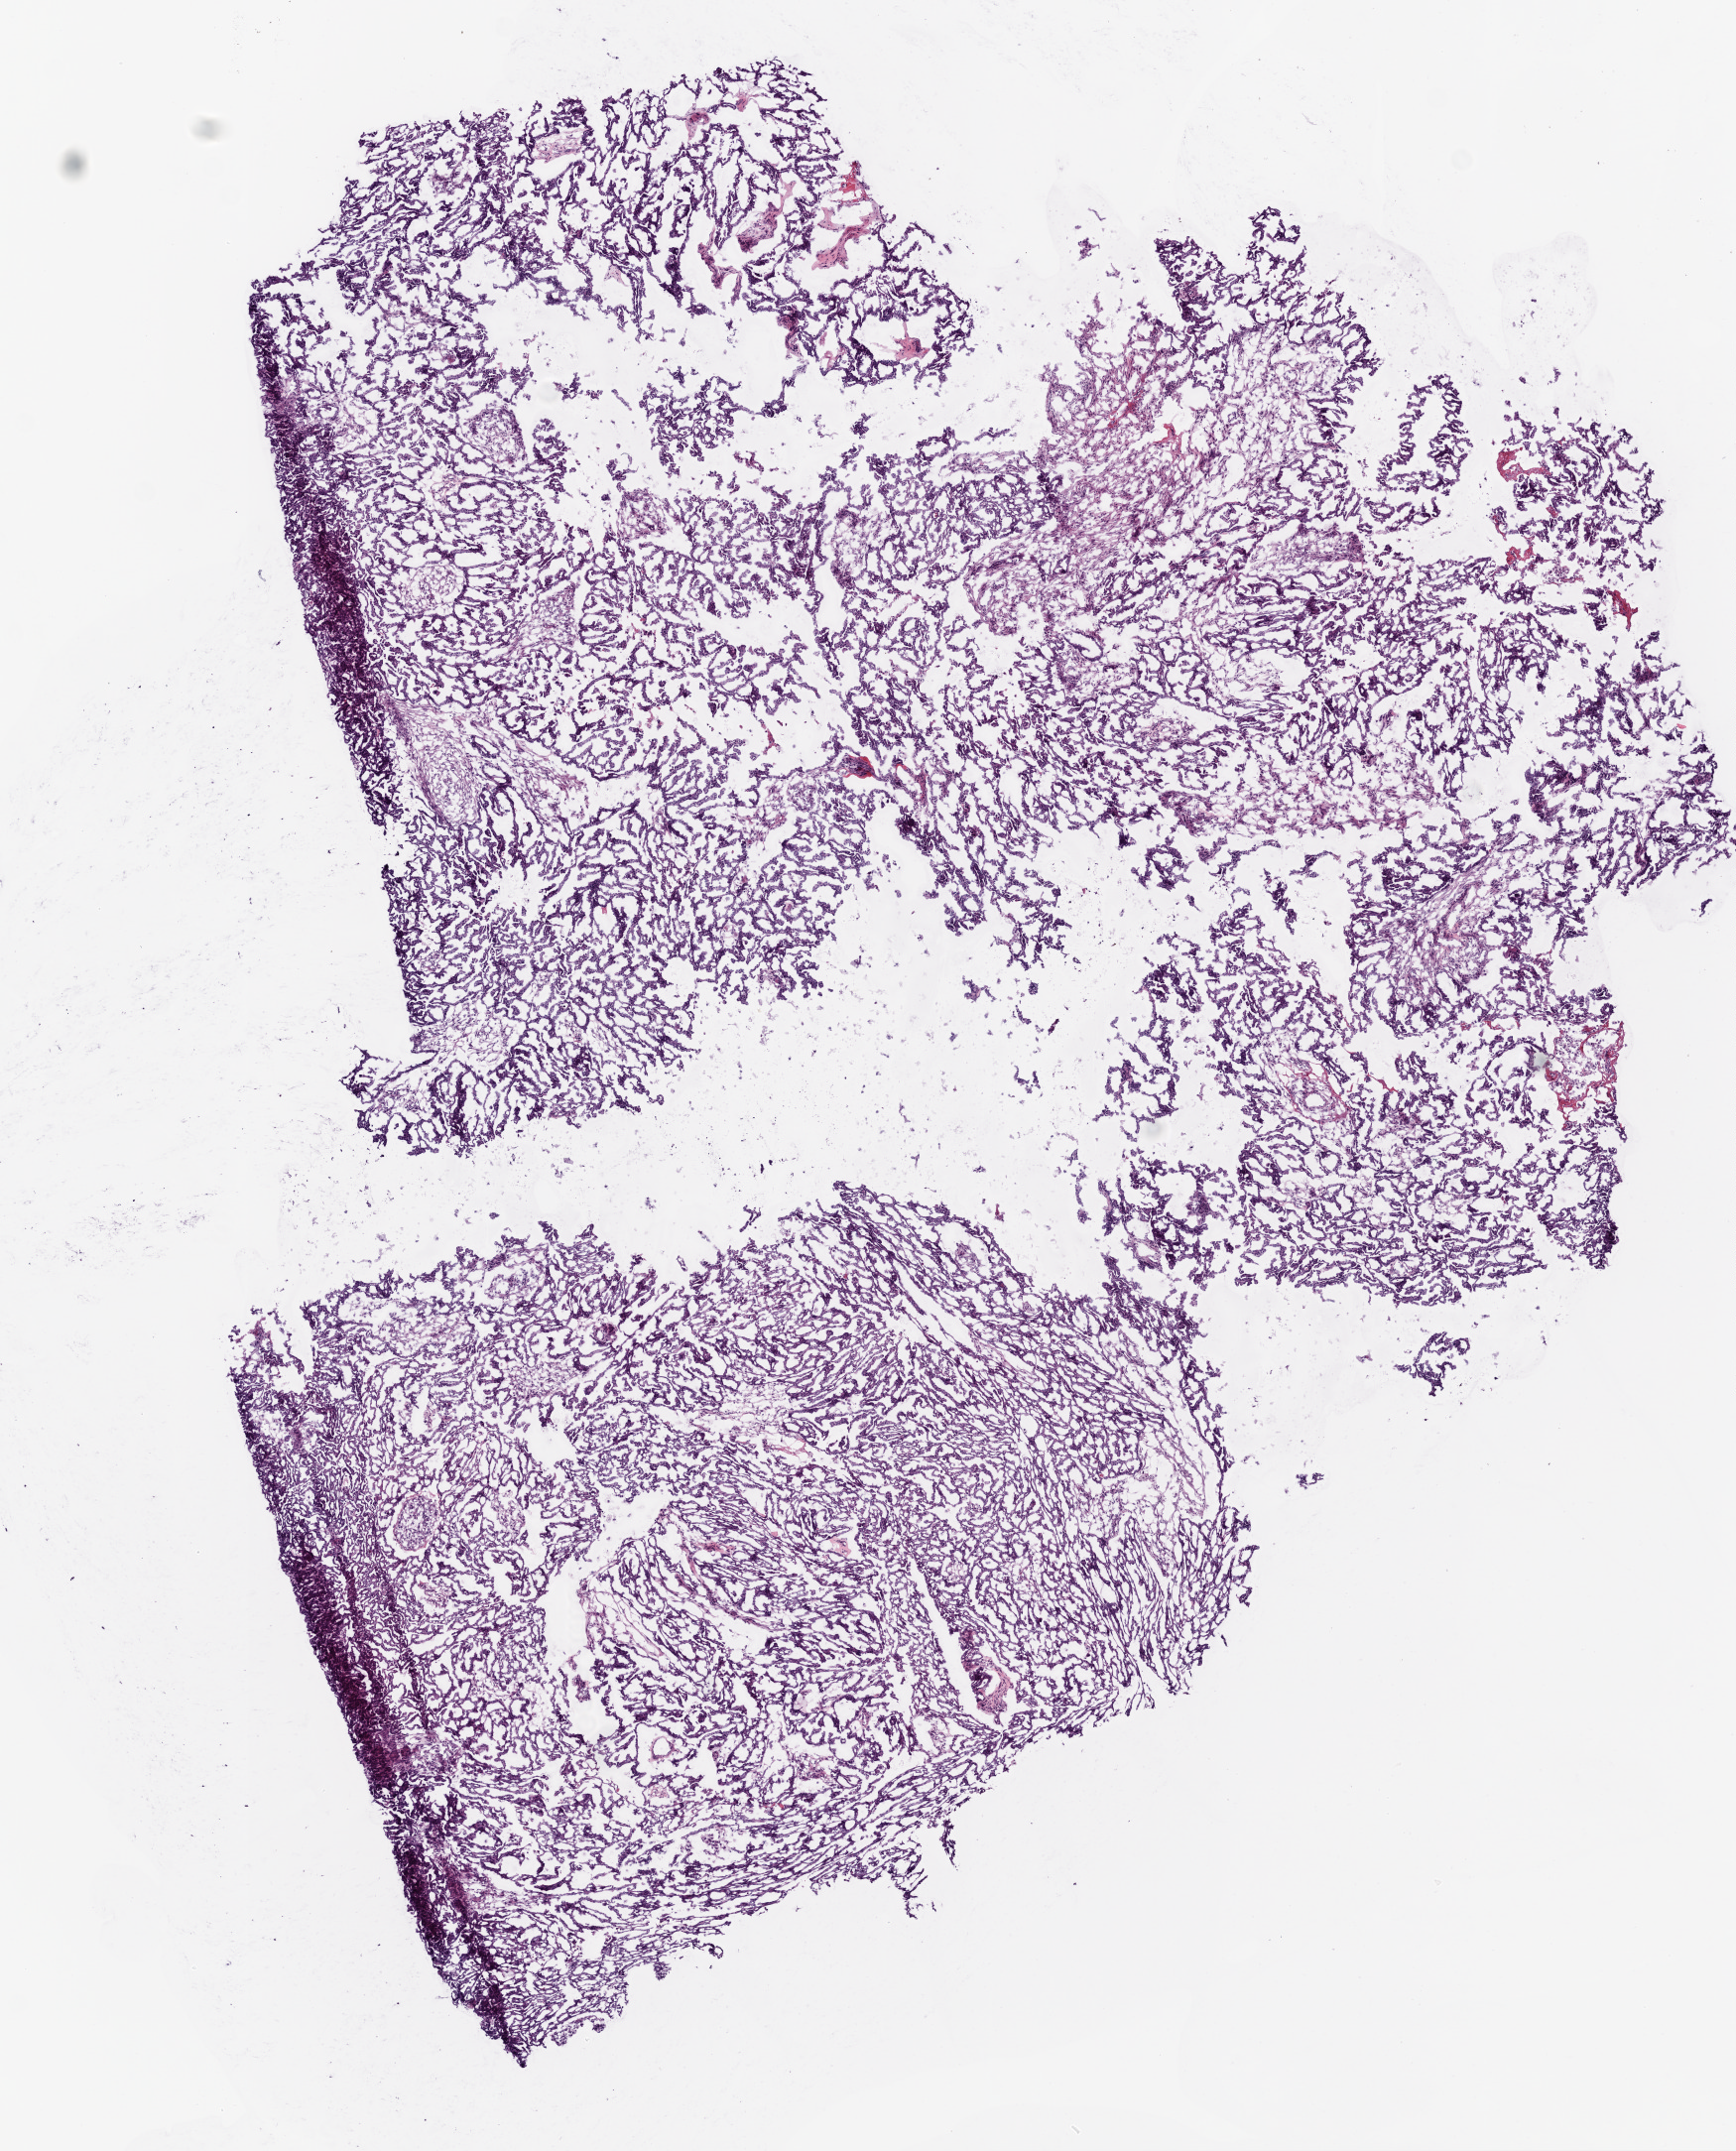
Digitized Hematoxylin and eosin (H&E) stained tissue section (whole slide) — low-resolution overview of the scanned area, about 7.0 x 8.7 mm (from a 20x scan); frozen section from the bottom of the tissue portion; primary tumour sample from the ovary. Female patient; age at initial diagnosis 49 years. Slide review estimates, as recorded: tumour cells 90%, tumour nuclei 90%.
Diagnosis: Serous cystadenocarcinoma, NOS.